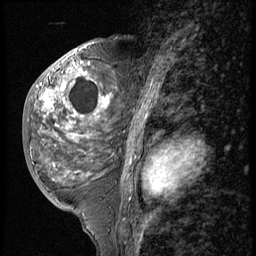
Breast MRI (dynamic contrast-enhanced), one sagittal slice; slice 28 of 56 in the series (ordered by position); 3 images stored at this slice position (order not interpretable as contrast timing); 1.5 T; TE 4.2 ms, TR 9 ms; 2.5 mm slice thickness; 256 × 256 image matrix, field of view 180 × 180 mm. Patient: female, 50 years. Case-level facts recorded for this patient, not image findings: setting: breast cancer imaged before/during neoadjuvant chemotherapy; receptor status: triple-negative.
Structures marked on this image (semi-automatically segmented with operator editing):
- analysis volume of interest (the breast-tissue region the enhancement analysis was run in; not a lesion): bounding box (x1, y1, x2, y2) in pixels: (25, 50, 118, 191)
- tumour enhancement mask (voxels above the 140 % enhancement threshold inside the analysis volume of interest): (43, 51, 109, 108)